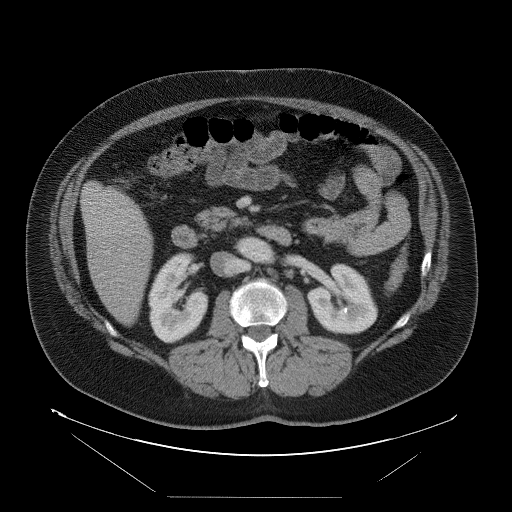
Contrast-enhanced abdominal CT, one axial slice; slice 31 of 114 in the series (ordered by position); intravenous contrast given; soft-tissue window (W 400 / L 40 HU); 512 × 512 image matrix. Male patient, age 61 years. From the clinical record (not read from this slice): diagnosis: colorectal cancer liver metastases, imaged before liver resection; multiple liver metastases: no; largest metastasis: 6.5 cm; disease in both lobes: yes.
Outlined on this slice (expert manual segmentation):
- liver: bounding box (x1, y1, x2, y2) in pixels: (82, 183, 154, 324)